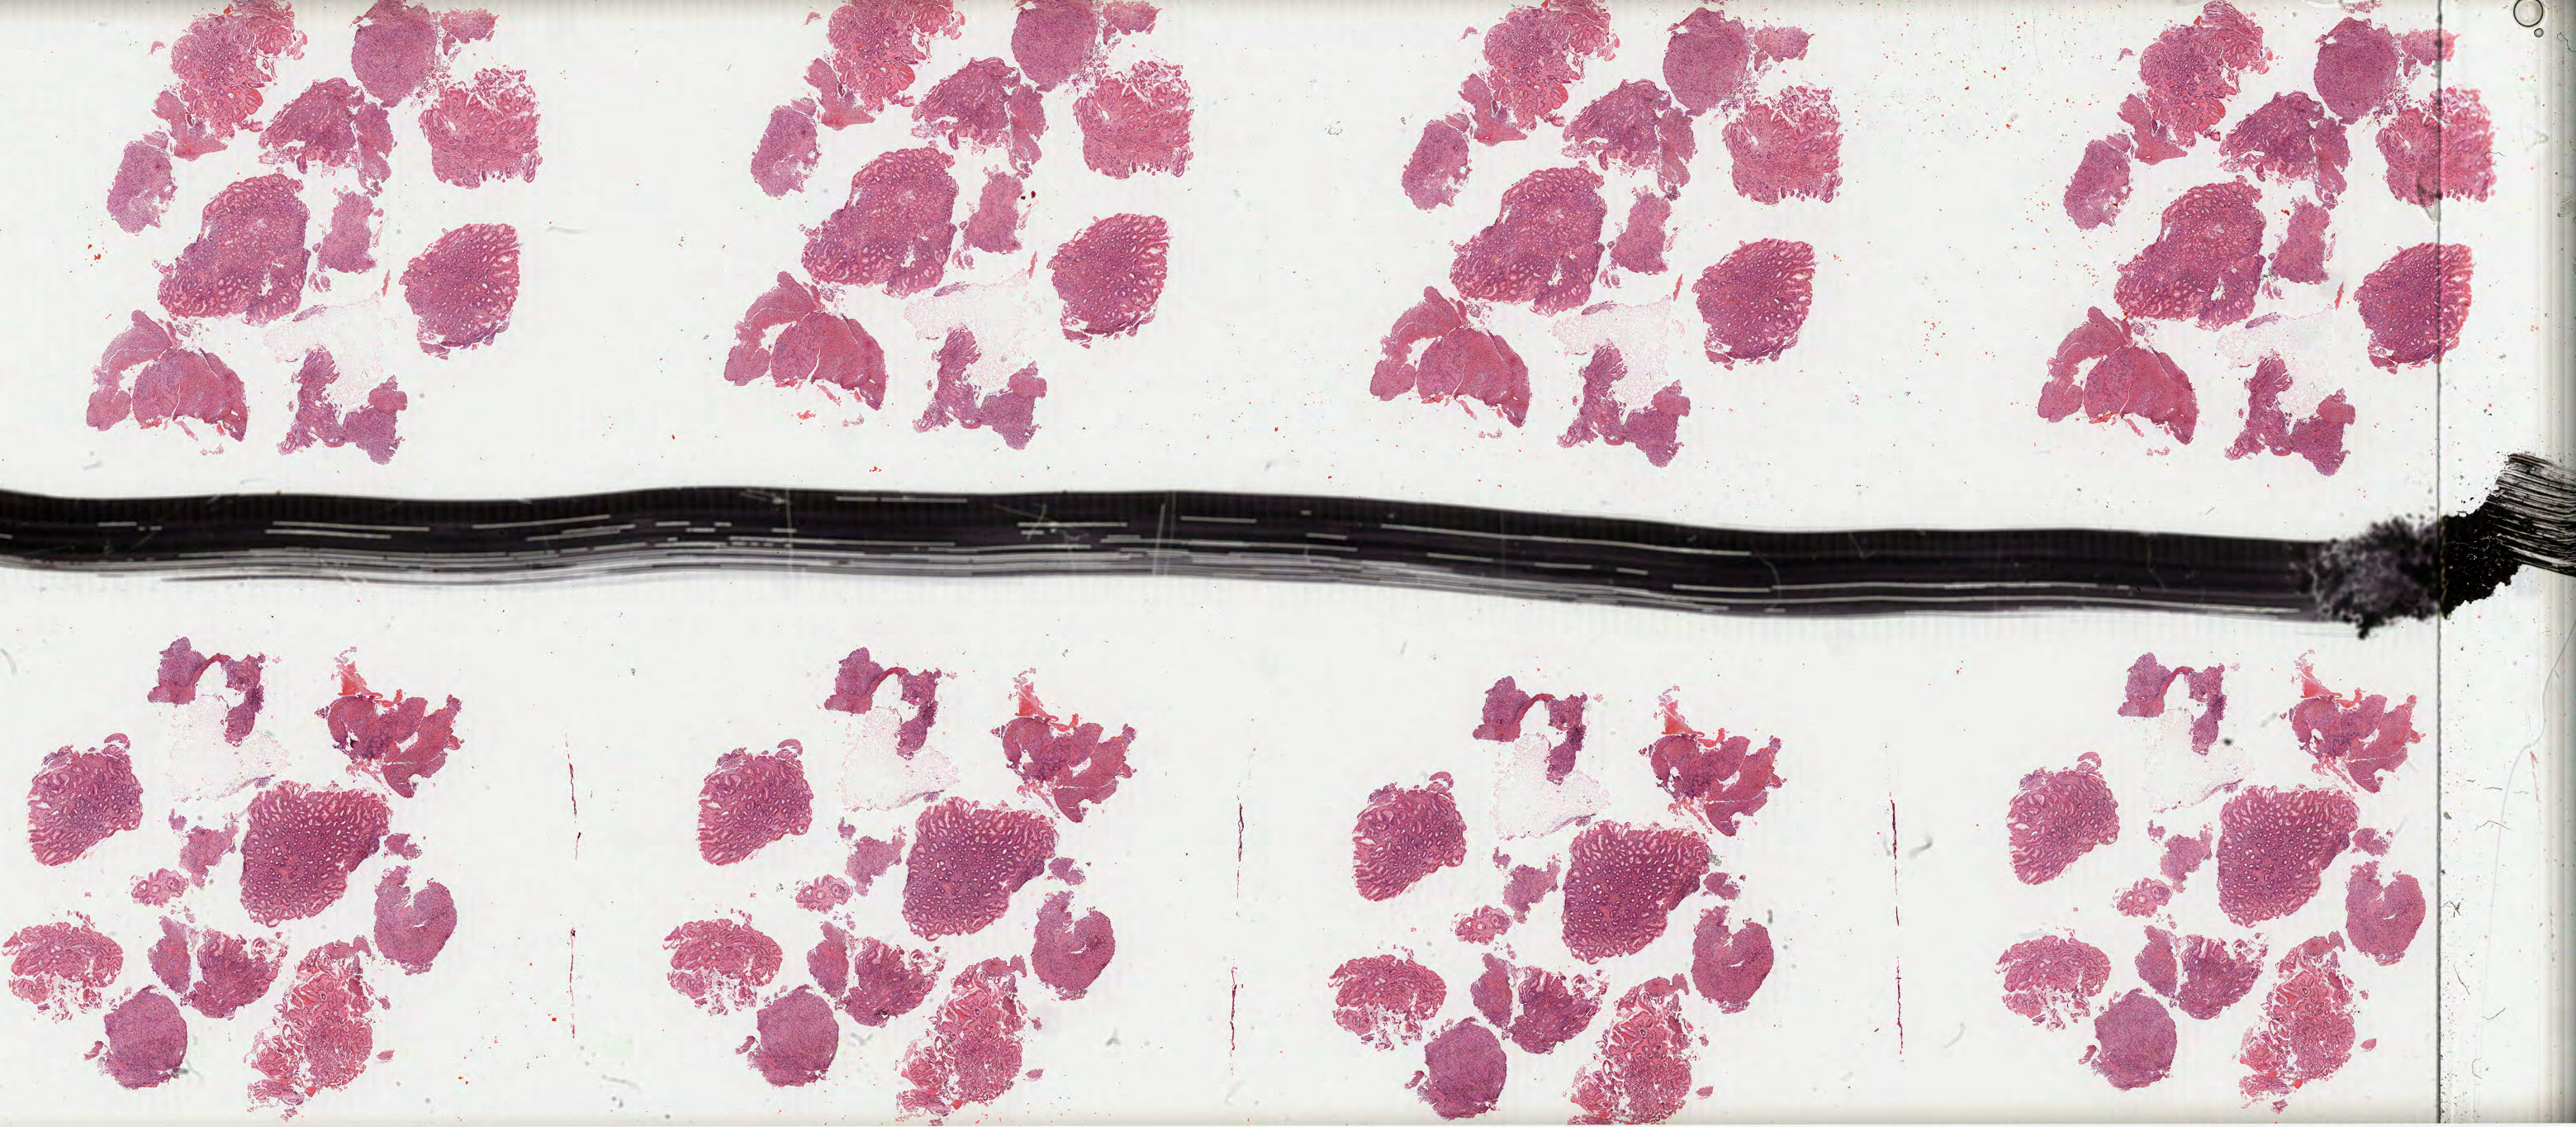
Digitized H&E tissue section (whole slide), whole scanned area (about 50.1 x 21.9 mm, from a 40x scan) shown as a low-resolution overview. Formalin-fixed paraffin-embedded (FFPE) diagnostic section. Primary tumour sample from the stomach. Patient: male, age at initial diagnosis 72 years. Histologic grade: G3 (poorly differentiated).
Histologic diagnosis: Adenocarcinoma, intestinal type (gastric antrum). AJCC pathologic stage: IIIB.